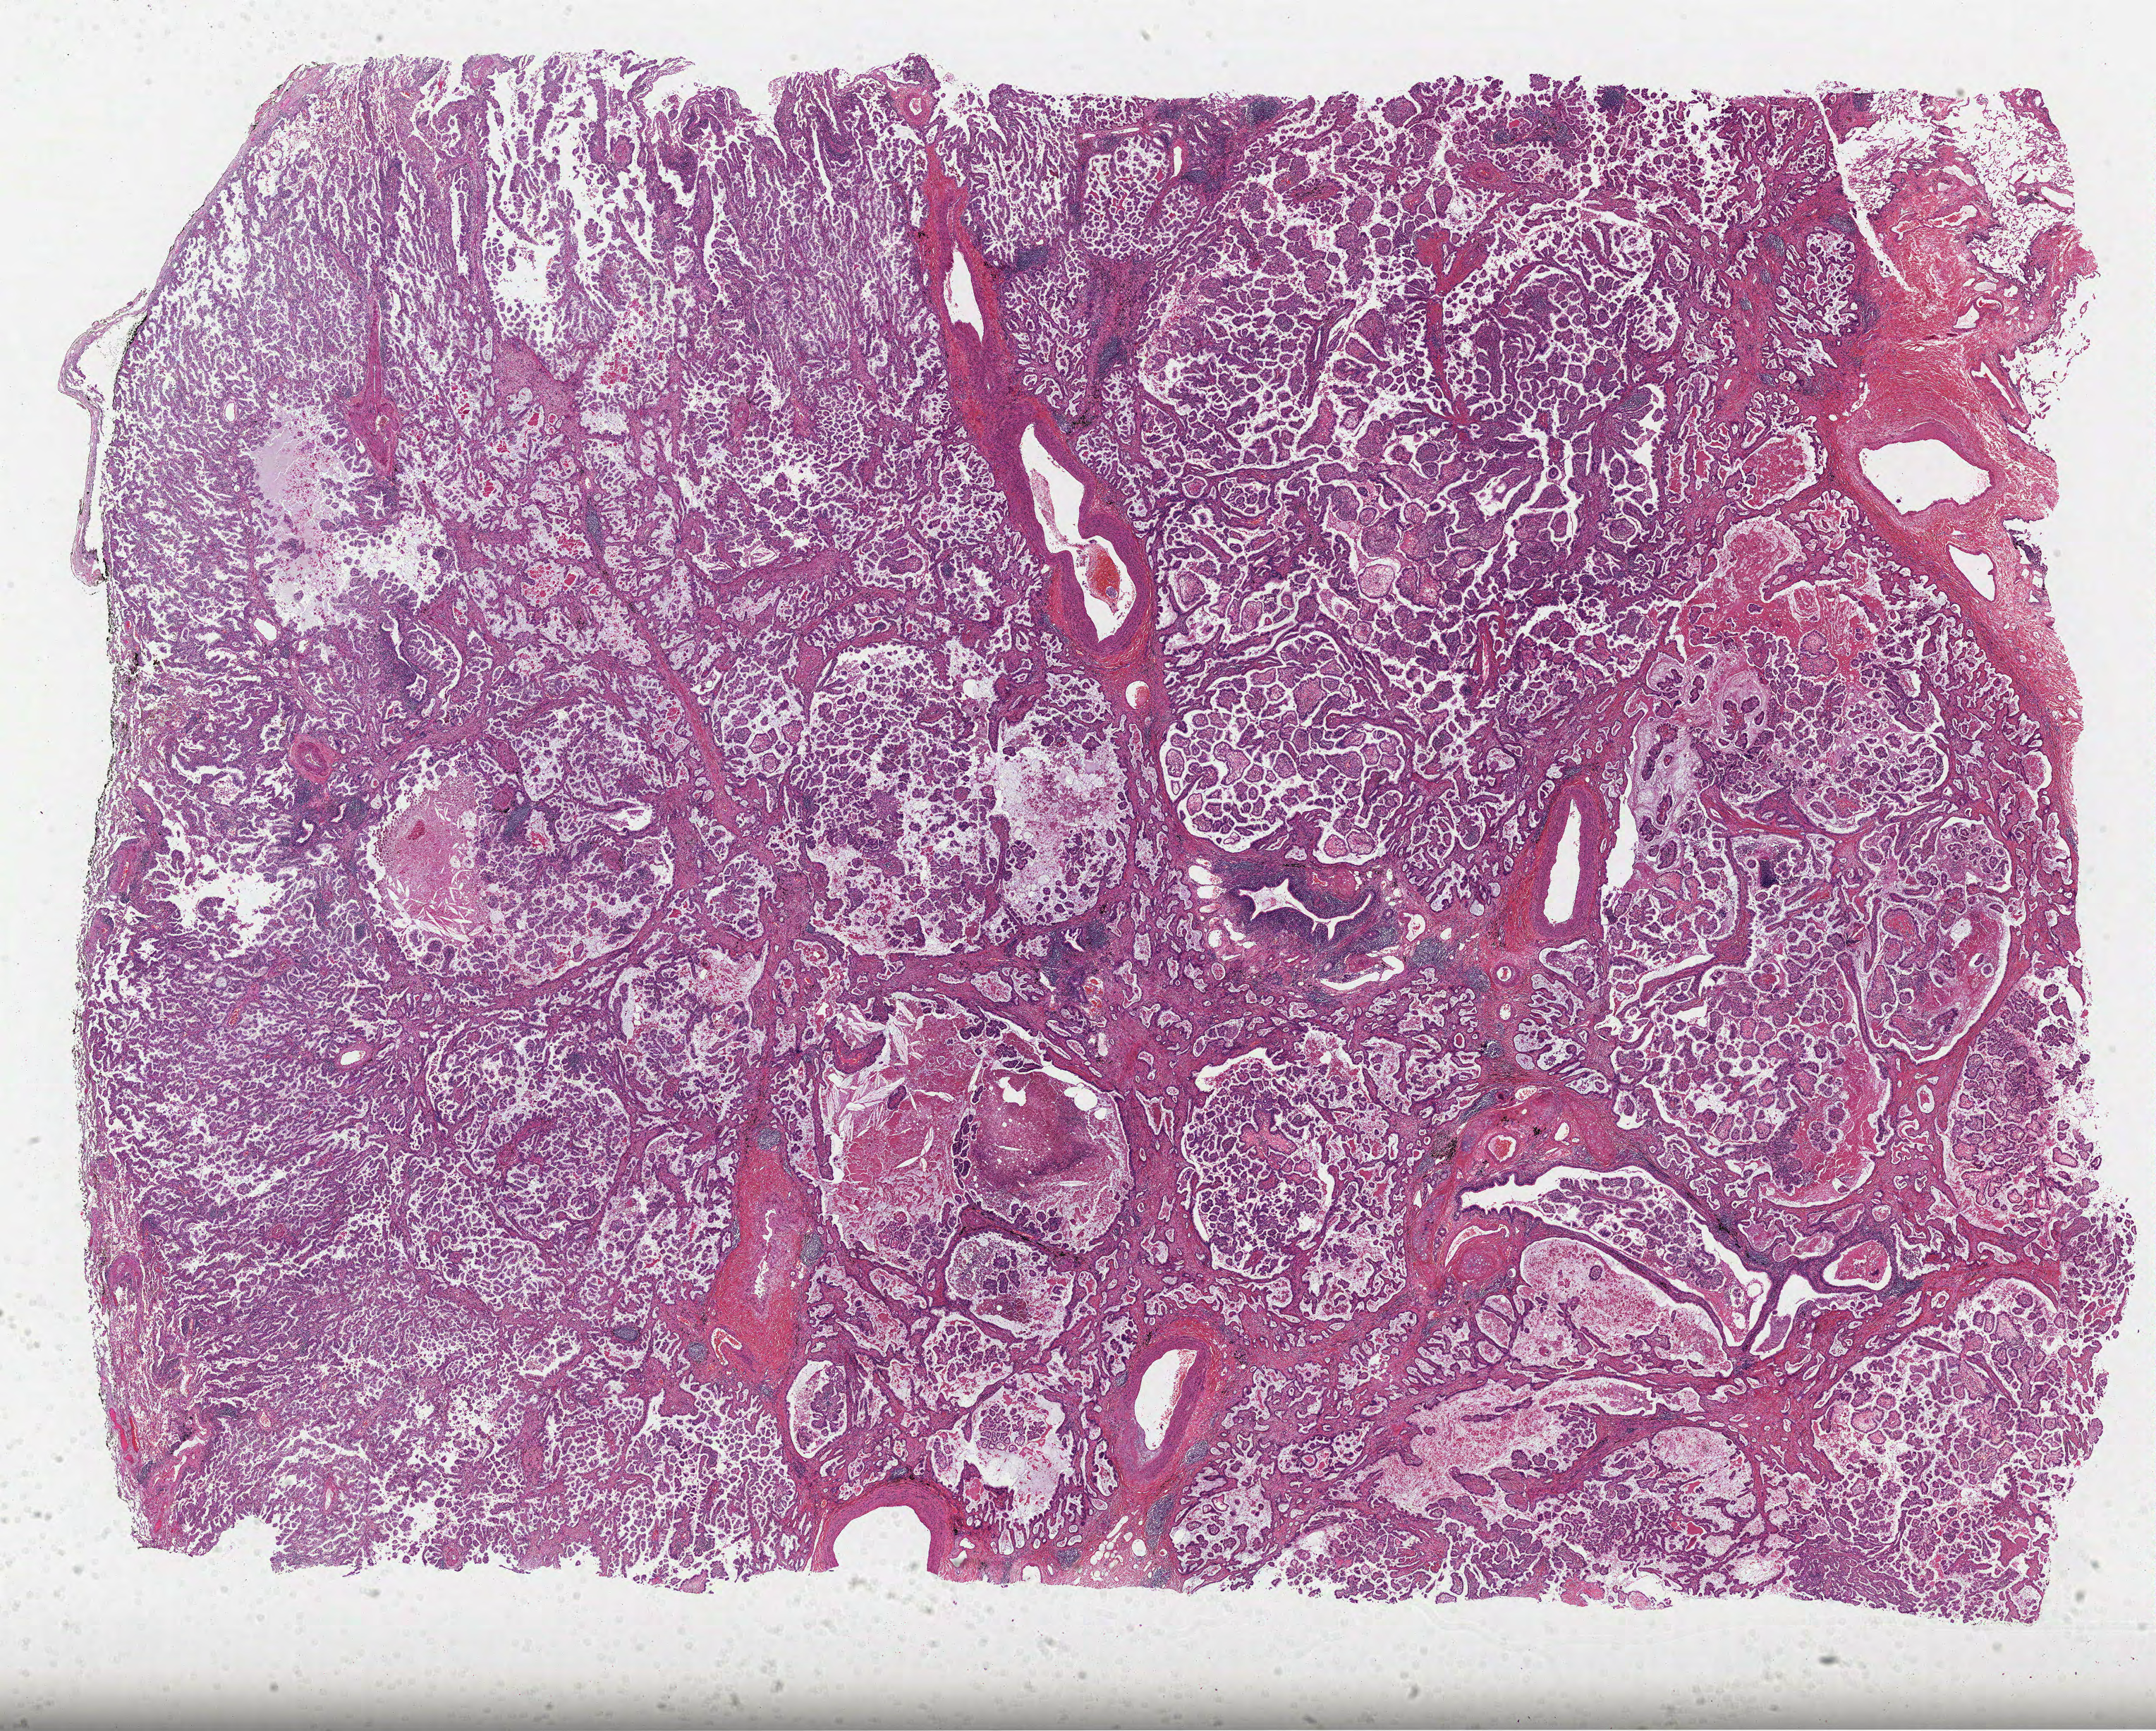
Digitized Hematoxylin and eosin (H&E) stained tissue section (whole slide), shown as a low-resolution overview of the whole scanned area (about 24.7 x 19.8 mm, slide scanned at 40x). Formalin-fixed paraffin-embedded (FFPE) diagnostic section. Lung, primary tumour sample. Patient: male, age at initial diagnosis 72 years.
Histologic diagnosis: Adenocarcinoma with mixed subtypes. Laterality: right. TNM: T2 N0 M0. AJCC pathologic stage: IB.